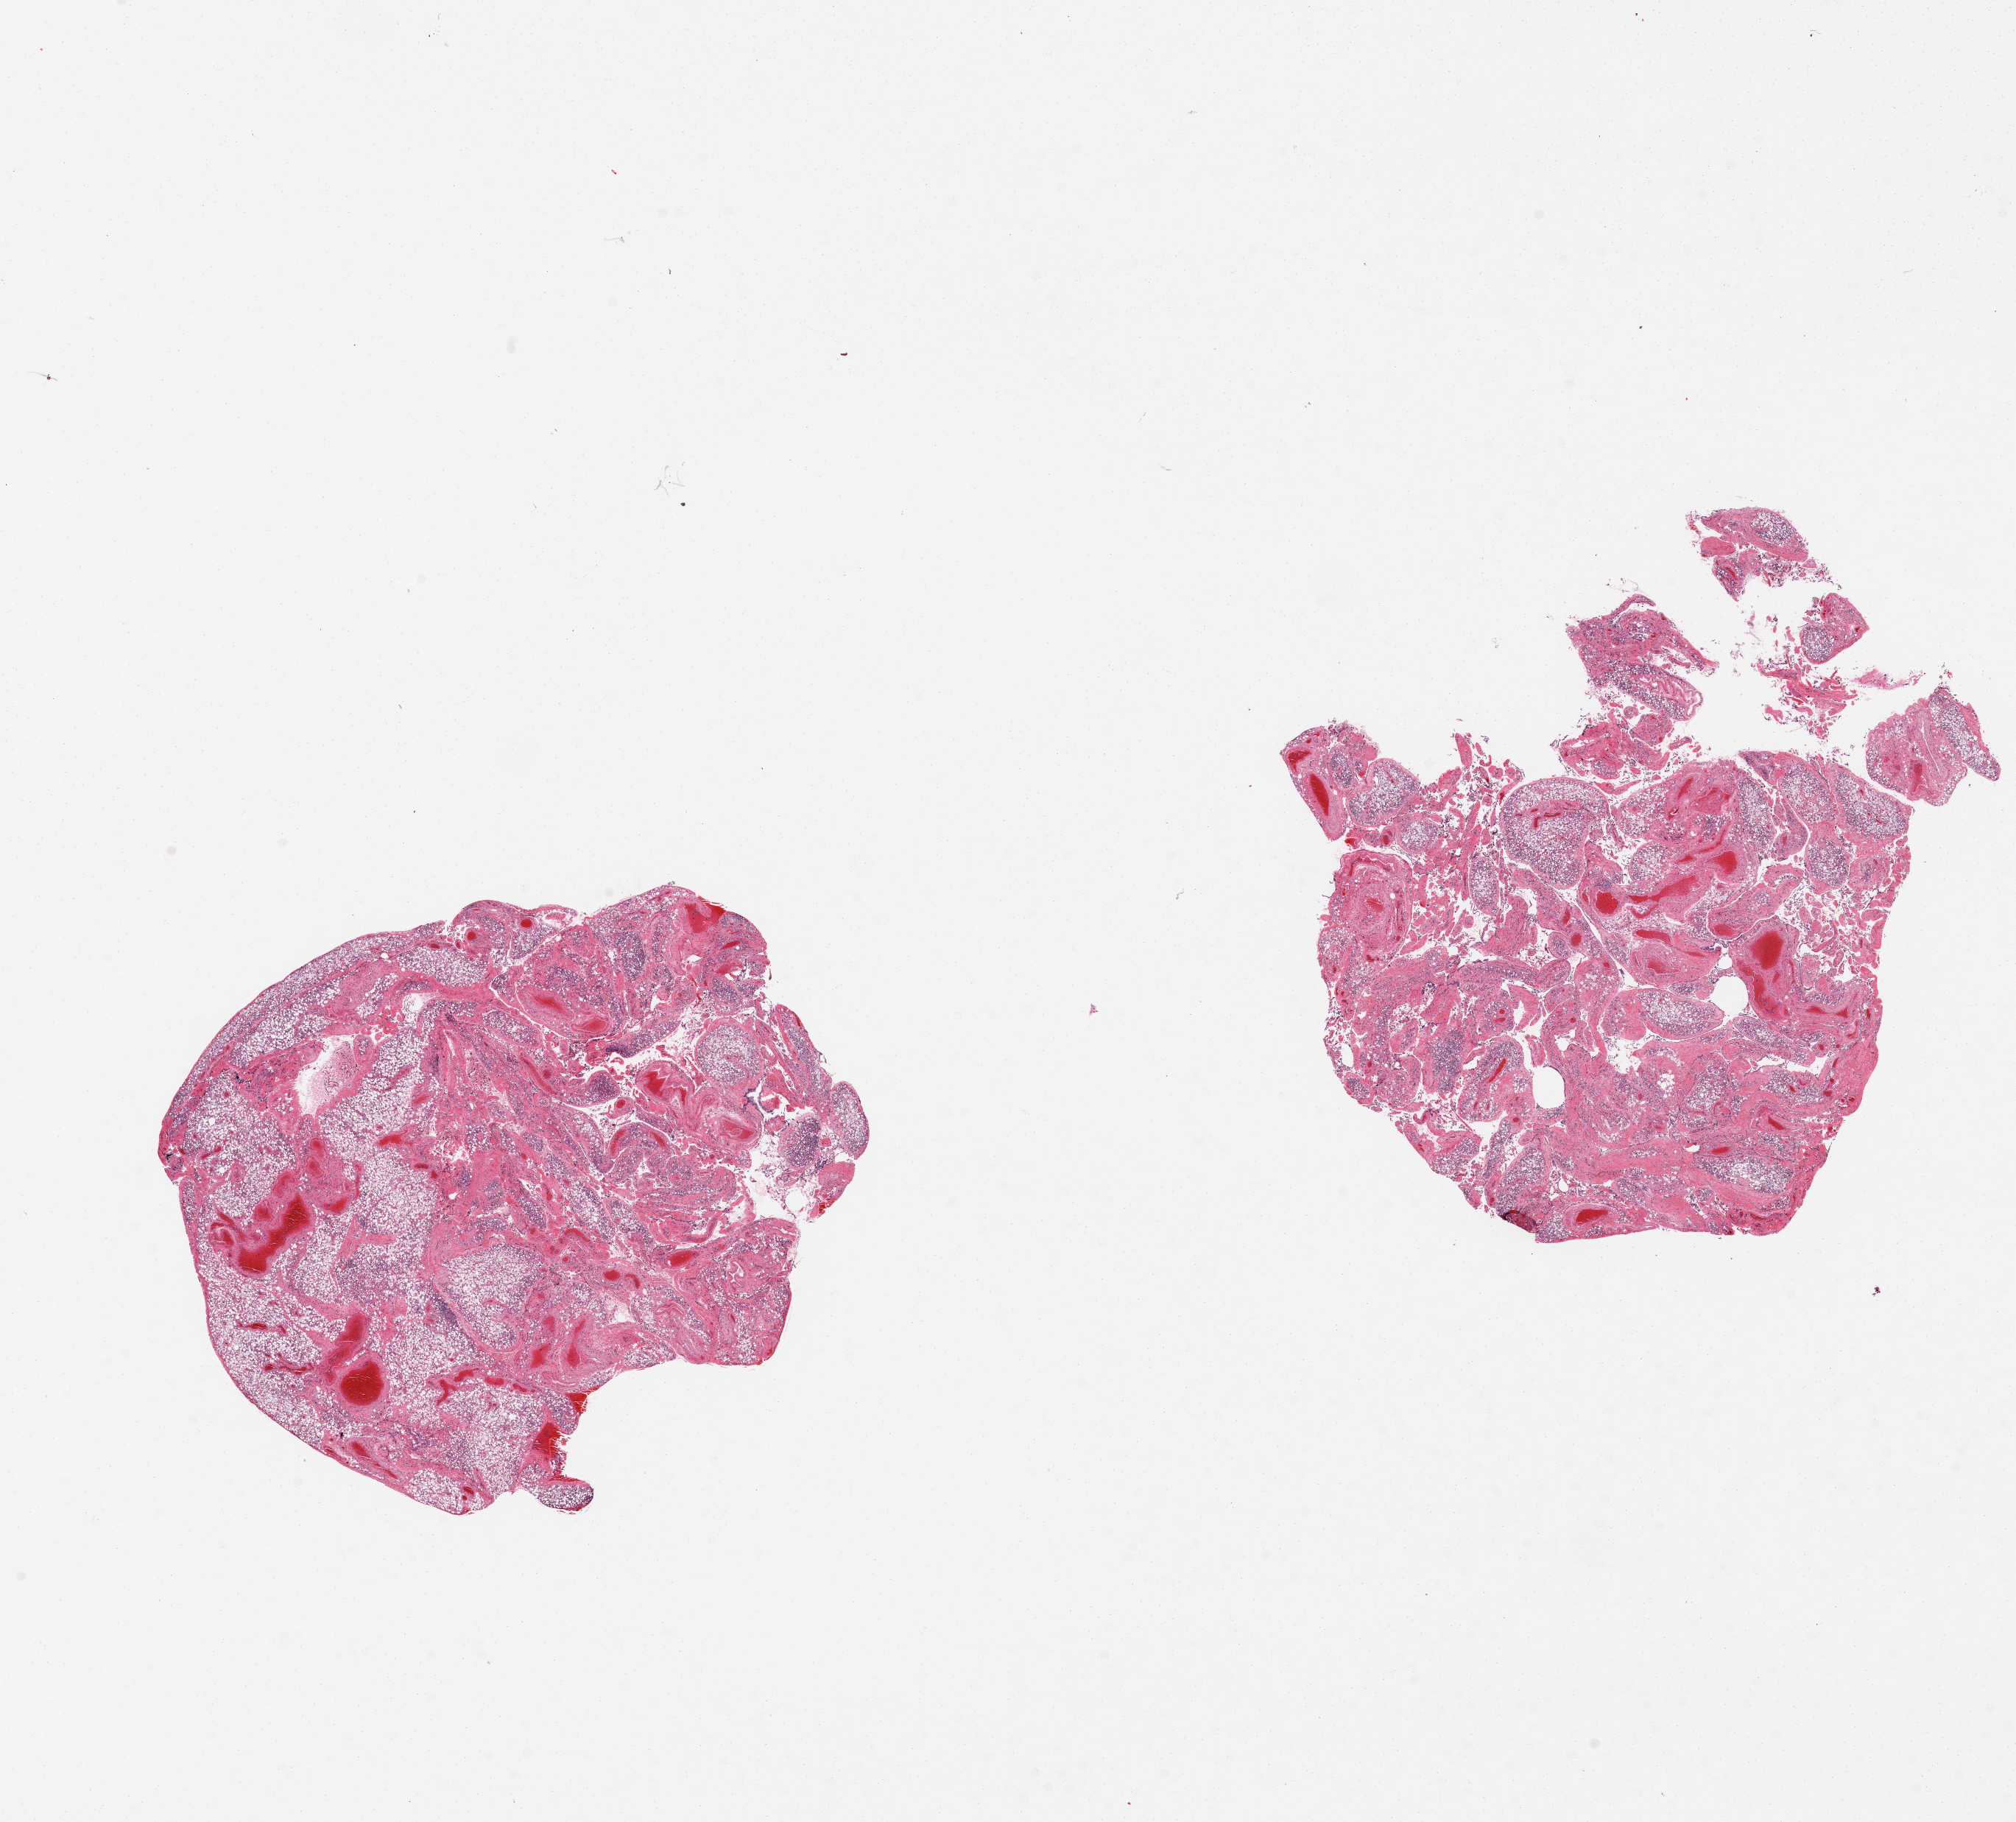
Haematoxylin and eosin whole-slide image, brightfield, shown as a low-resolution overview of the whole scanned area (about 21.7 x 19.6 mm), PAXgene-fixed, paraffin-embedded tissue, target tissue: omentum, donor tissue sample. Donor: male.
* pathologist's review note for this sample: 2 pieces, extensive fibrosis/inflammation, mesothelial hyperplasia secondary to ascites (a few foci)